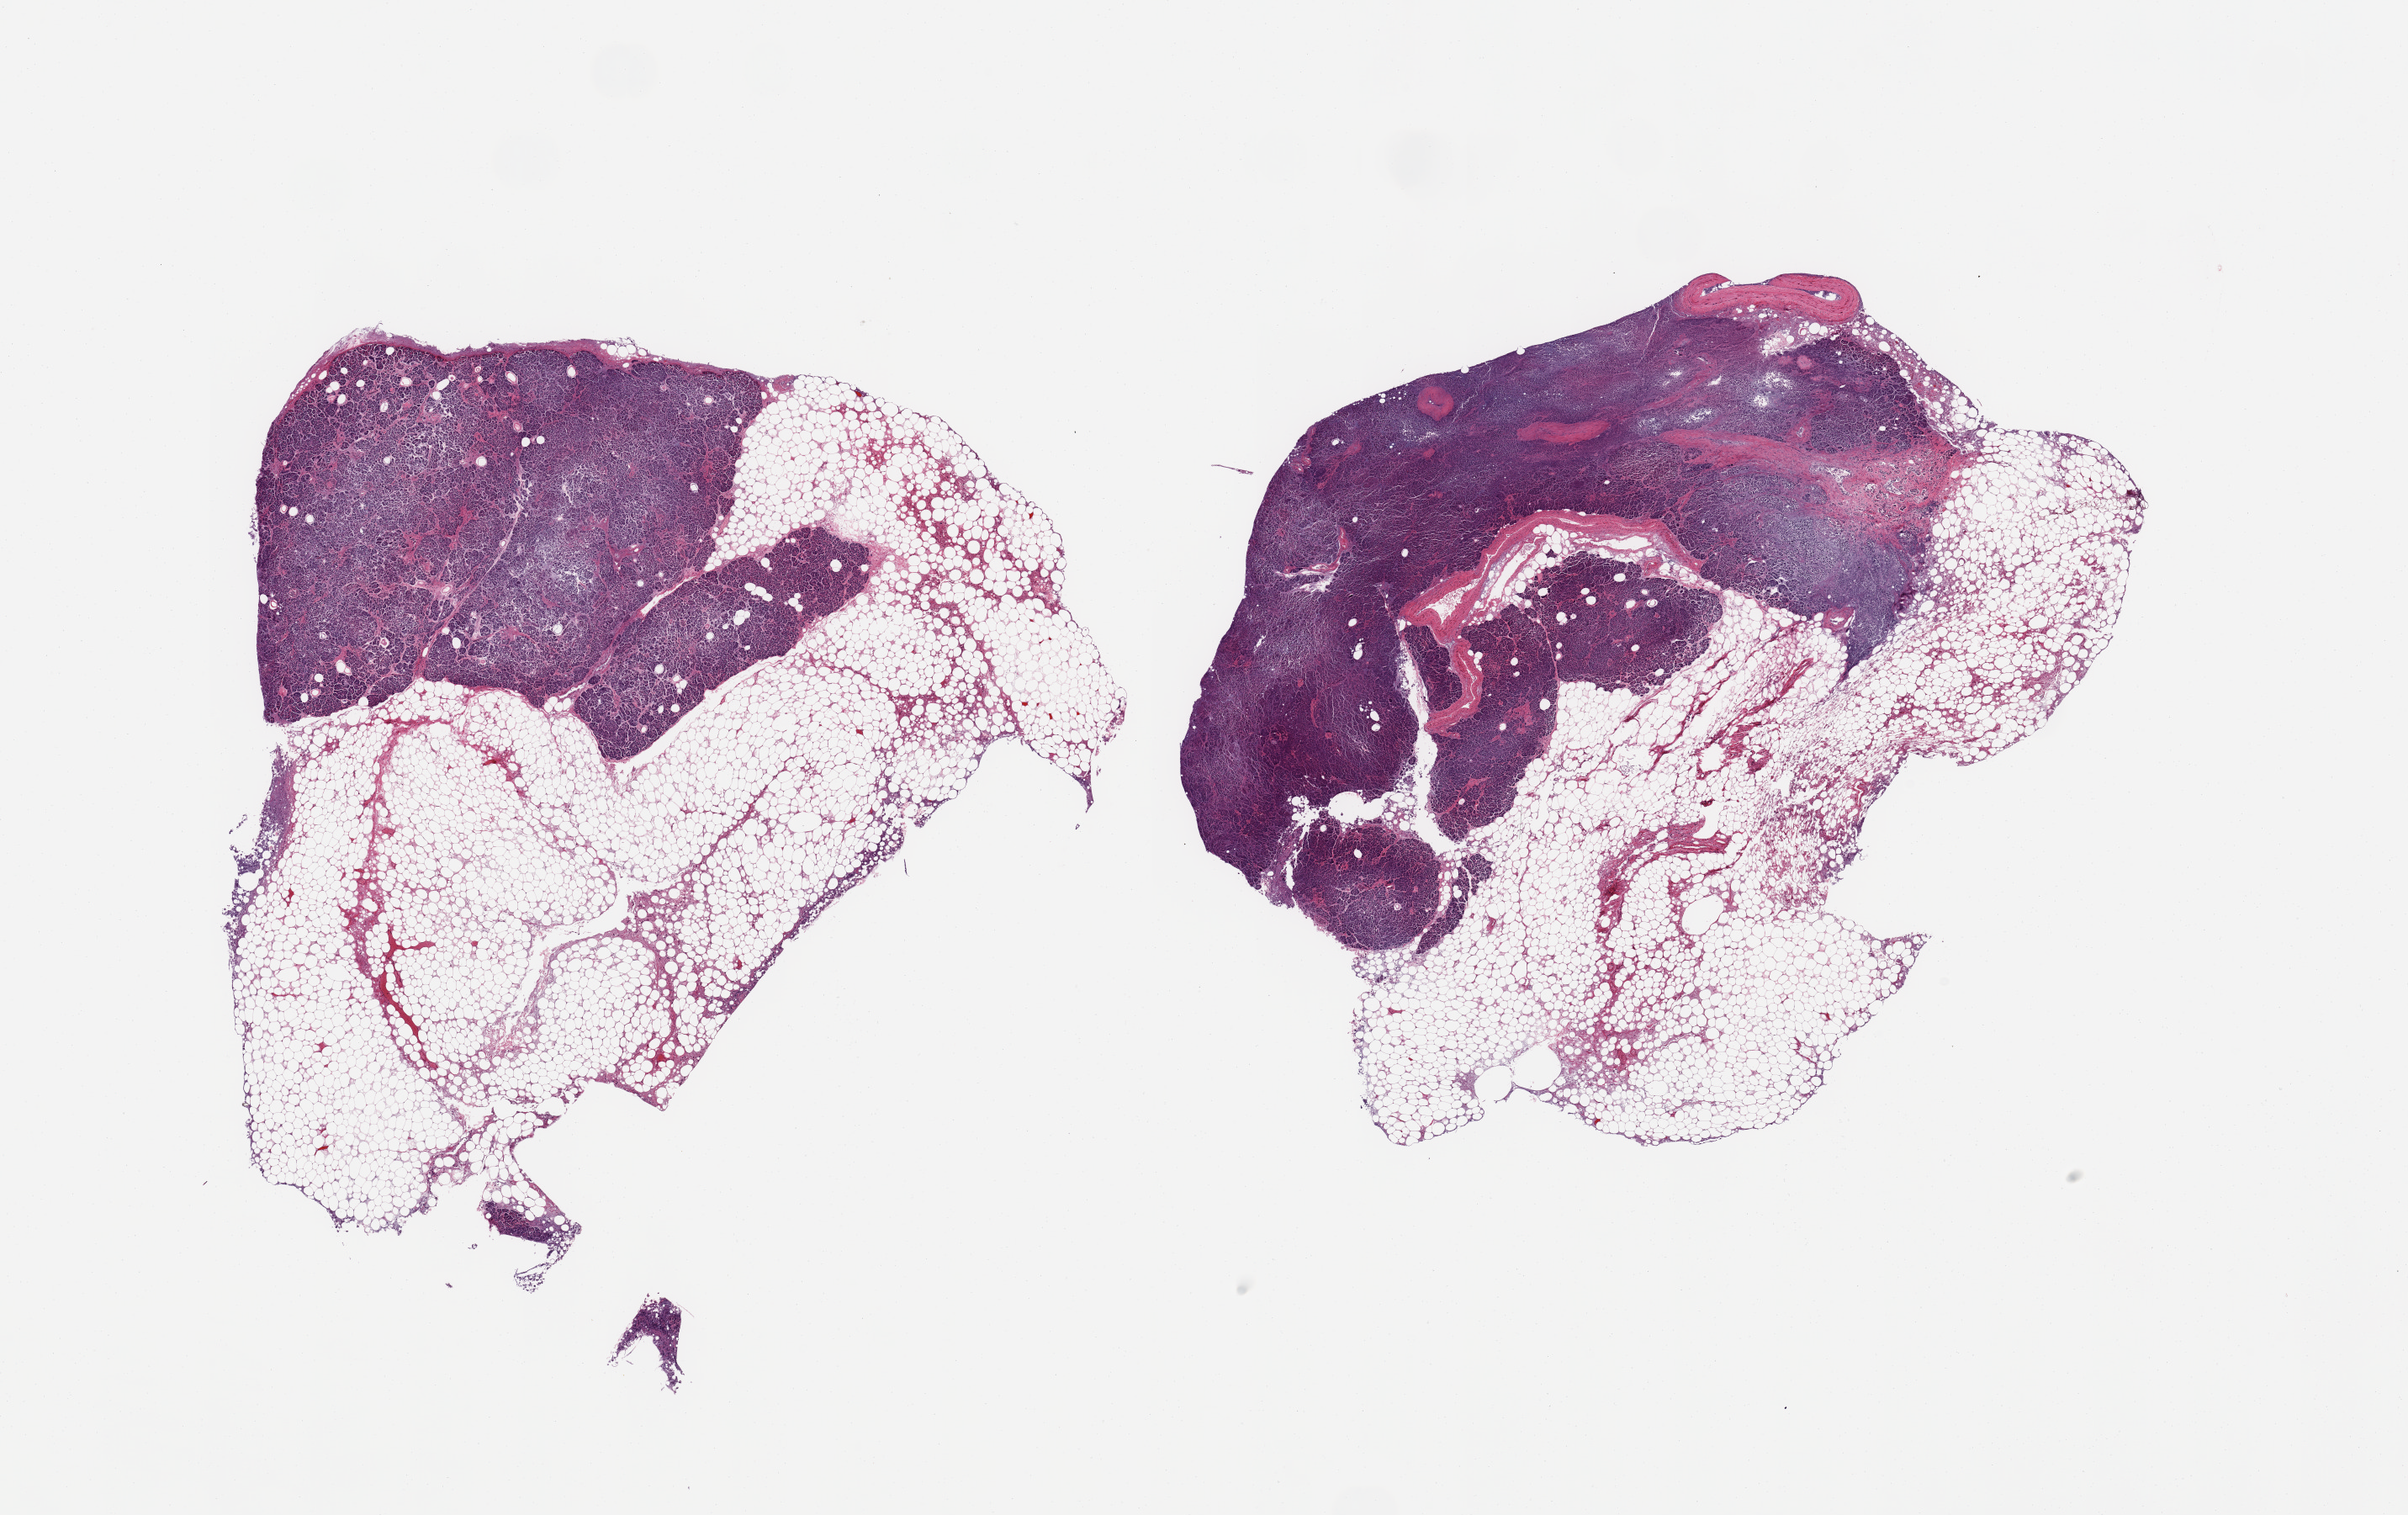
Digitized hematoxylin and eosin (H&E)-stained section — whole scanned area (about 22.6 x 14.2 mm, slide scanned at 20x) shown as a low-resolution overview; PAXgene-fixed, paraffin-embedded tissue; target tissue: pancreas; donor tissue sample. Donor: male.
Reviewer comment on this tissue sample: 2 pieces, moderately advanced saponification, islets not visible; ~50% parenchyma, ~50% adherent/interstitial fat.